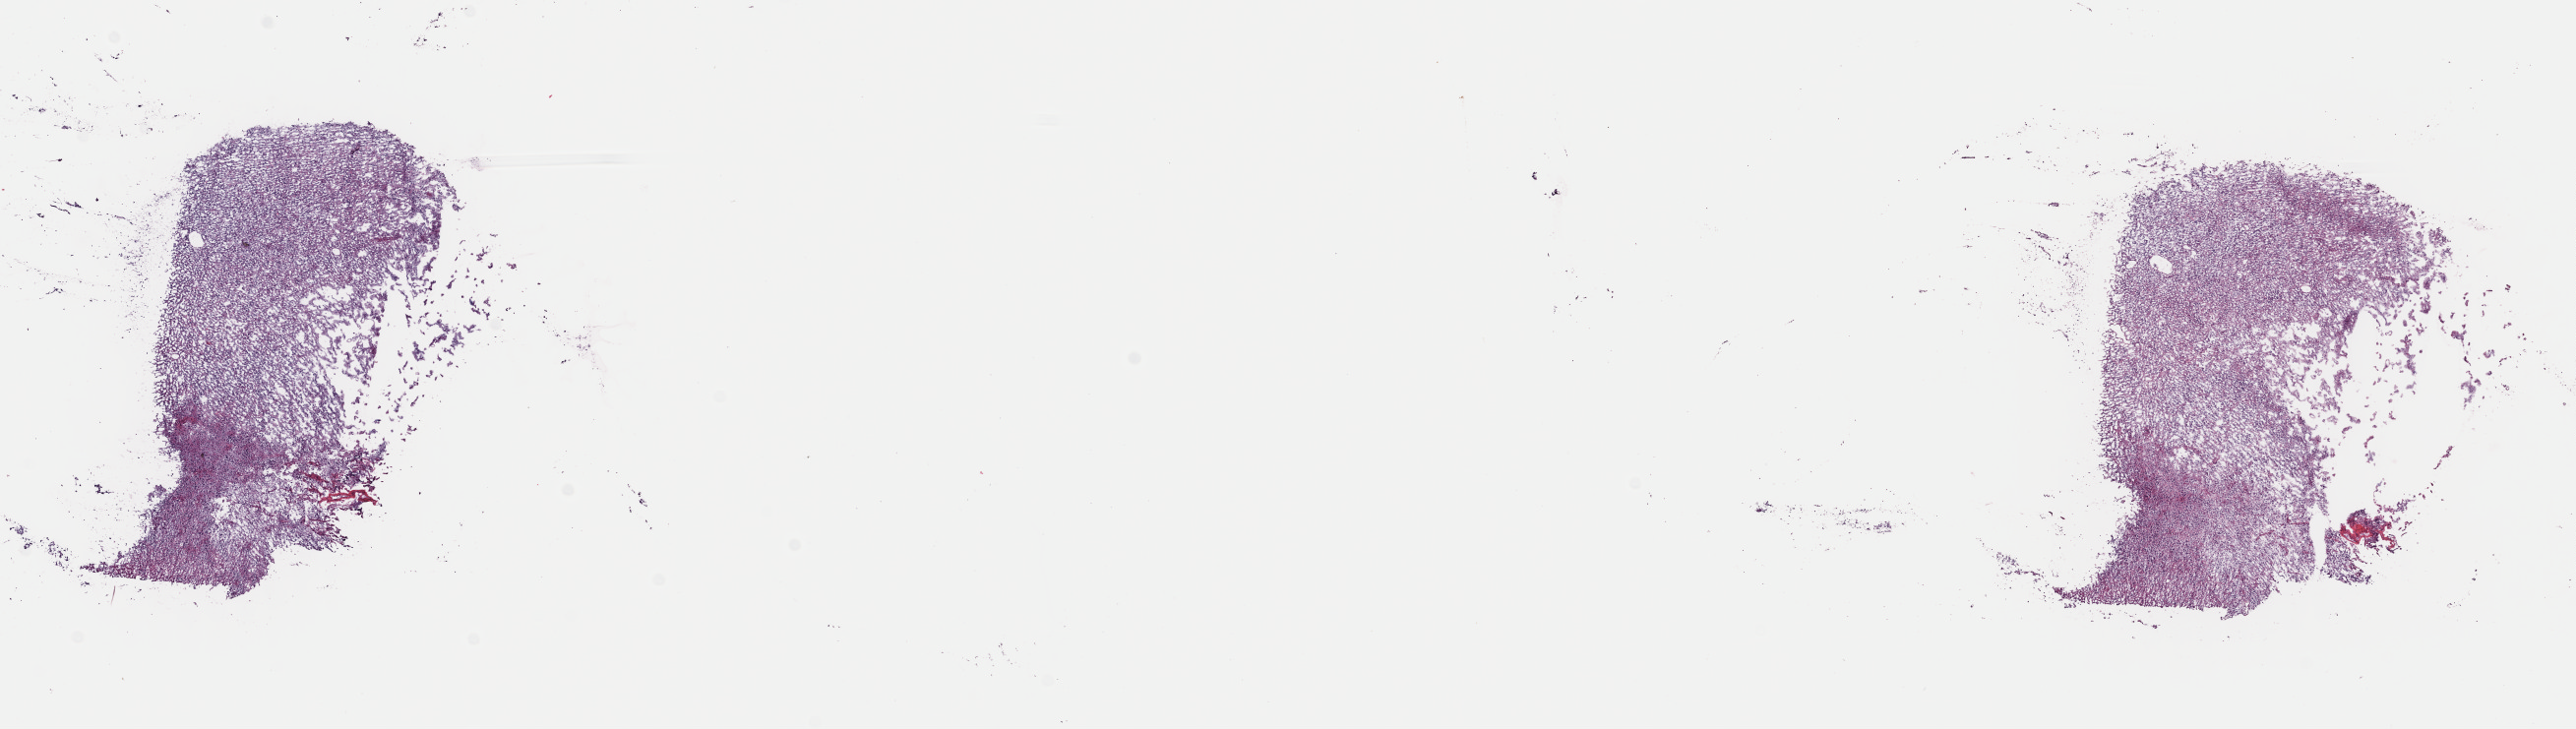
Digitized H&E-stained tissue section (whole slide) — a low-resolution overview of the entire scanned area, about 20.7 x 5.8 mm, frozen section from the top of the tissue portion, sample: primary tumour, brain. Male, age 40 years at initial diagnosis. Histologic grade: G3 (poorly differentiated). Slide review estimates, as recorded: tumour cells 70%, tumour nuclei 80%, normal cells 10%, stromal cells 20%, necrosis 0%. Inflammatory infiltration, as recorded: lymphocyte infiltration 0%, monocyte infiltration 0%, neutrophil infiltration 0%.
Histologic diagnosis: Oligodendroglioma, anaplastic (cerebrum).